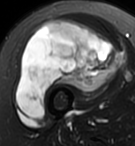
MRI of an extremity soft-tissue mass, one axial slice; position 56 of 95 along the scan axis; T2-weighted fat-saturated; MR volume resampled by the dataset authors to the PET/CT grid (not the native acquisition matrix); 3.27 mm slice thickness; 135 × 146 image matrix. Female patient. Case-level facts recorded for this patient, not image findings: histological type: pleiomorphic undifferentiated sarcoma; grade: high; site of the primary tumour: right quadricep.
Annotated regions visible in this slice (expert contour drawn on MRI and transferred to this co-registered scan by the dataset authors):
- gross tumour volume including surrounding oedema: bounding box <16,18,122,119> (left, top, right, bottom; pixels)
- gross tumour volume (mass): <16,18,122,119>